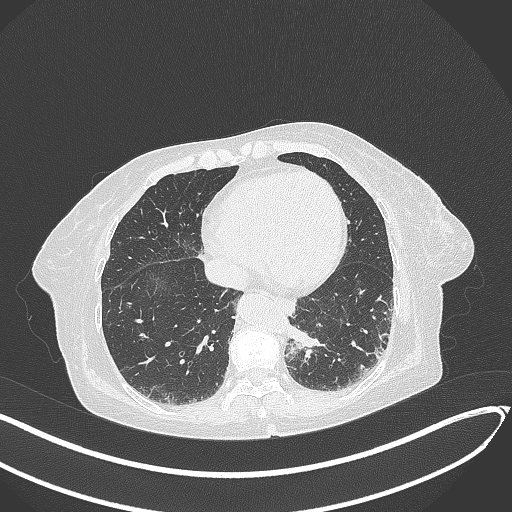
Chest CT, one axial slice; position 62 of 324 along the scan axis; reconstruction kernel B70f; 120 kVp; lung window (W 1500 / L -600 HU); 1 mm slice thickness; 512 × 512 image matrix, field of view 400 × 400 mm. Female patient, age 82 years. From the clinical record (not read from this slice): clinical TNM (as recorded): T1b N0 M1.
Structures marked on this image (bounding box drawn by a radiologist):
- lung tumour (recorded histology: adenocarcinoma): bounding box (x1, y1, x2, y2) in pixels: (287, 321, 323, 353)